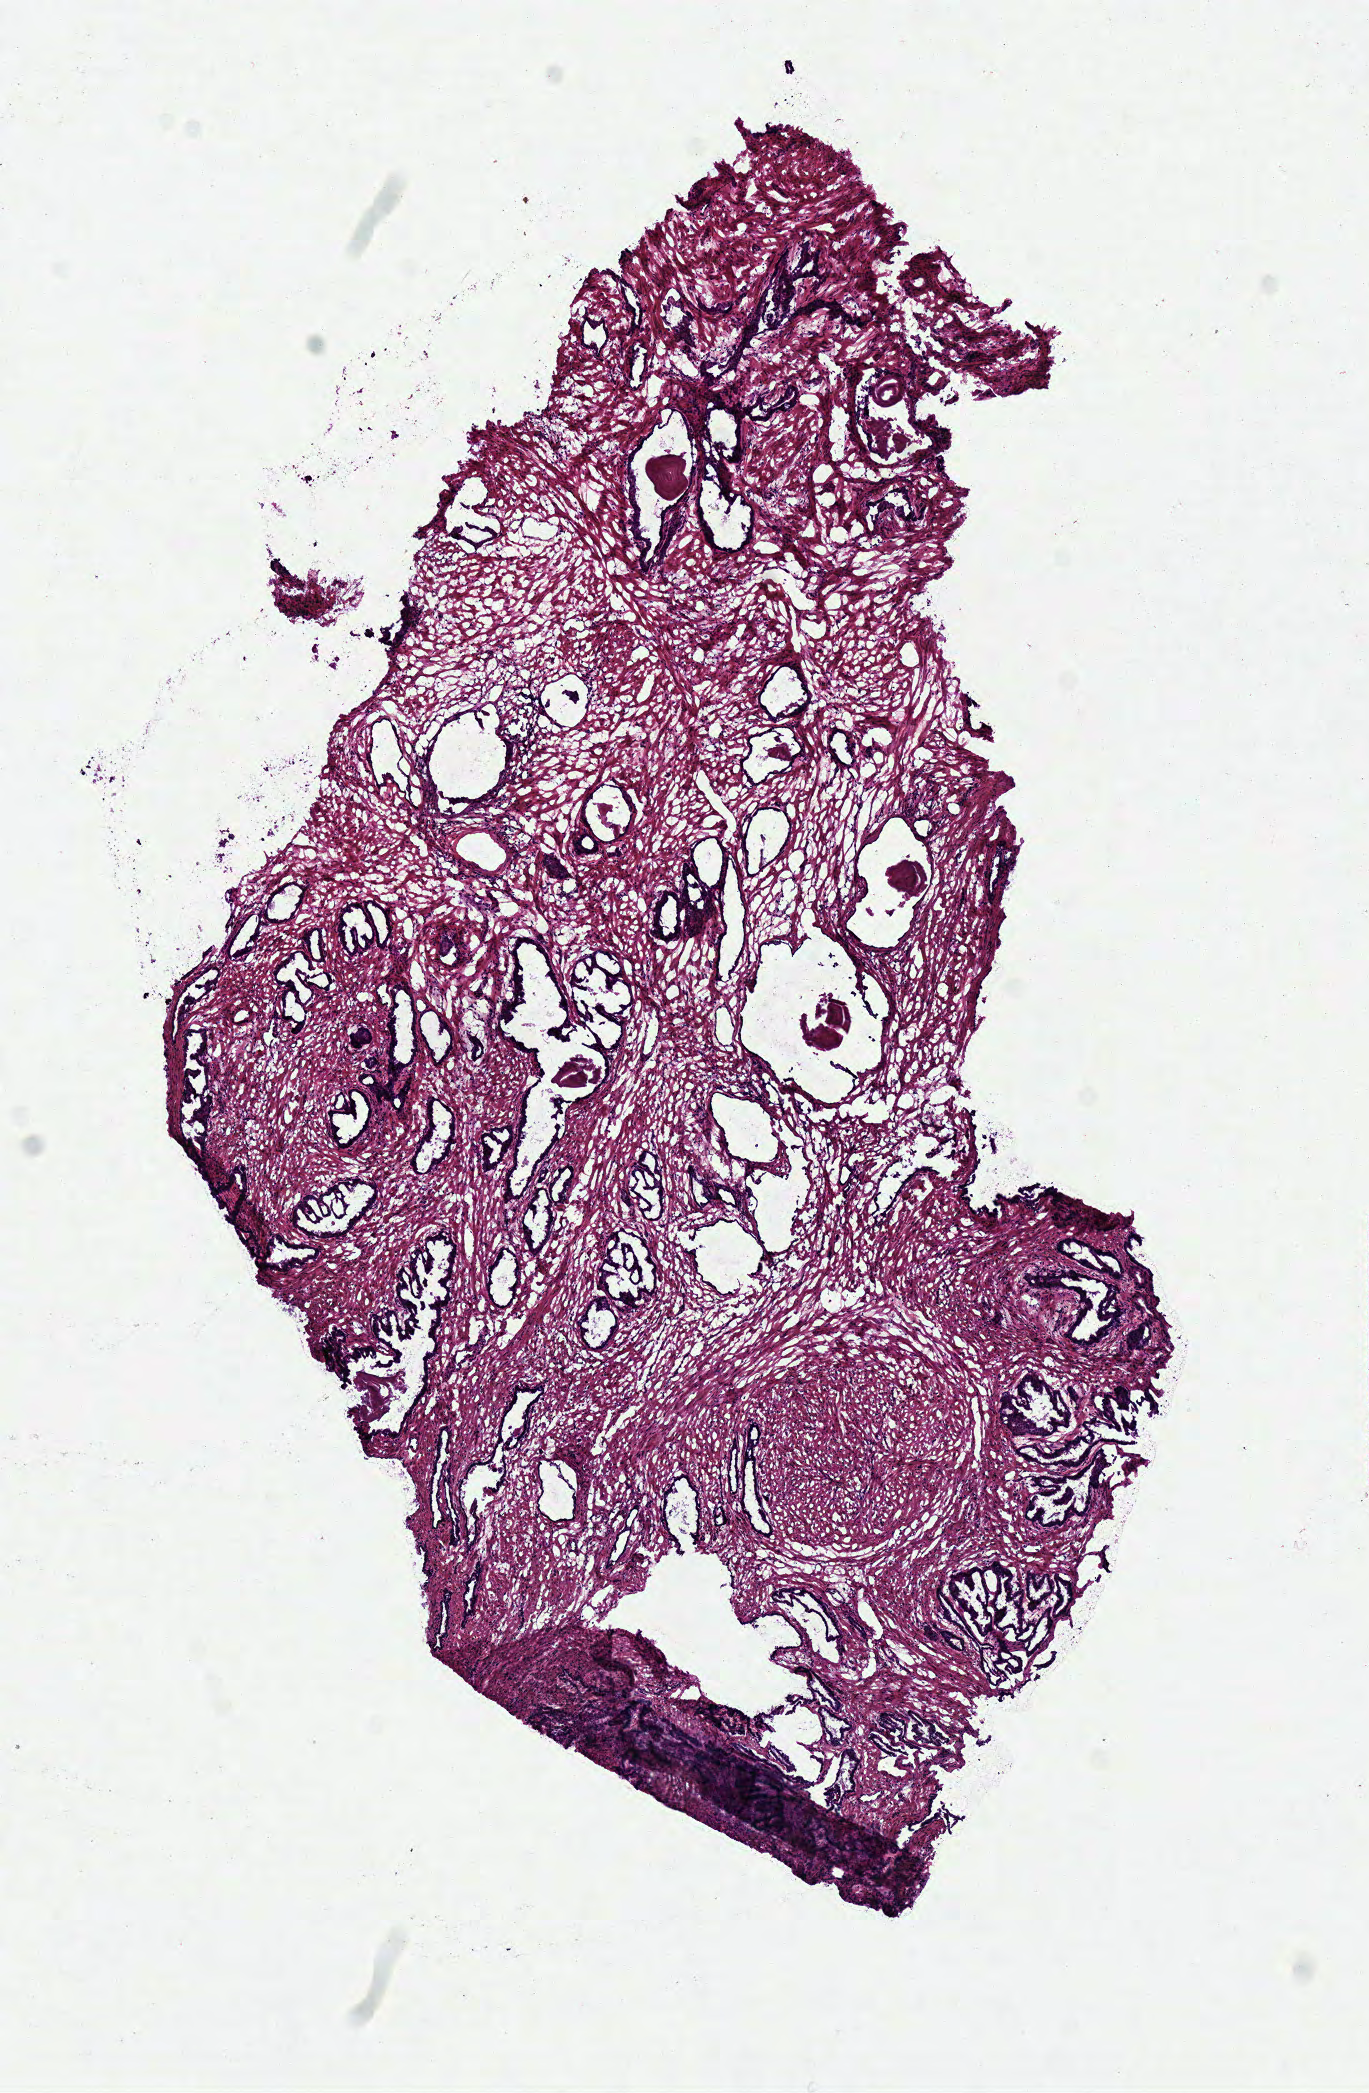
Digitized H&E-stained tissue section (whole slide) — a low-resolution overview of the entire scanned area, about 5.4 x 8.2 mm, frozen section from the top of the tissue portion, sample: solid tissue normal (non-tumour tissue), prostate. Patient: male, age at initial diagnosis 58 years.
This section: solid tissue normal (non-tumour) sample from the same patient. Patient diagnosis: Acinar cell carcinoma (prostate gland).